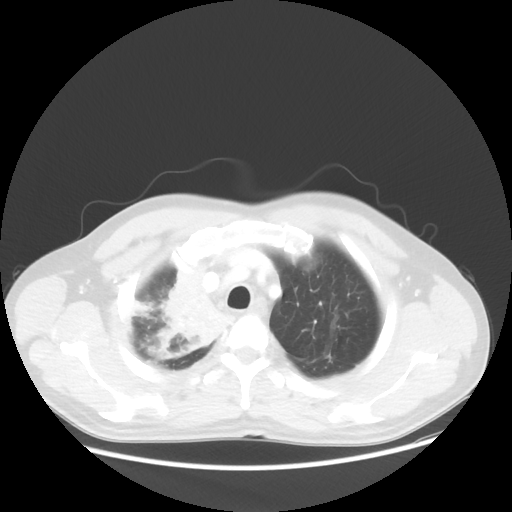
Chest CT, one axial slice; position 45 of 56 along the scan axis; 100 kVp; lung window (W 1500 / L -600 HU); 5 mm slice thickness; 512 × 512 image matrix. Male patient, age 60 years. From the clinical record (not read from this slice): clinical TNM (as recorded): T2a N1 M0.
Structures marked on this image (rectangle marked by the reading radiologist):
- lung tumour (recorded histology: squamous cell carcinoma): bounding box (x1, y1, x2, y2) in pixels: (154, 257, 243, 360)